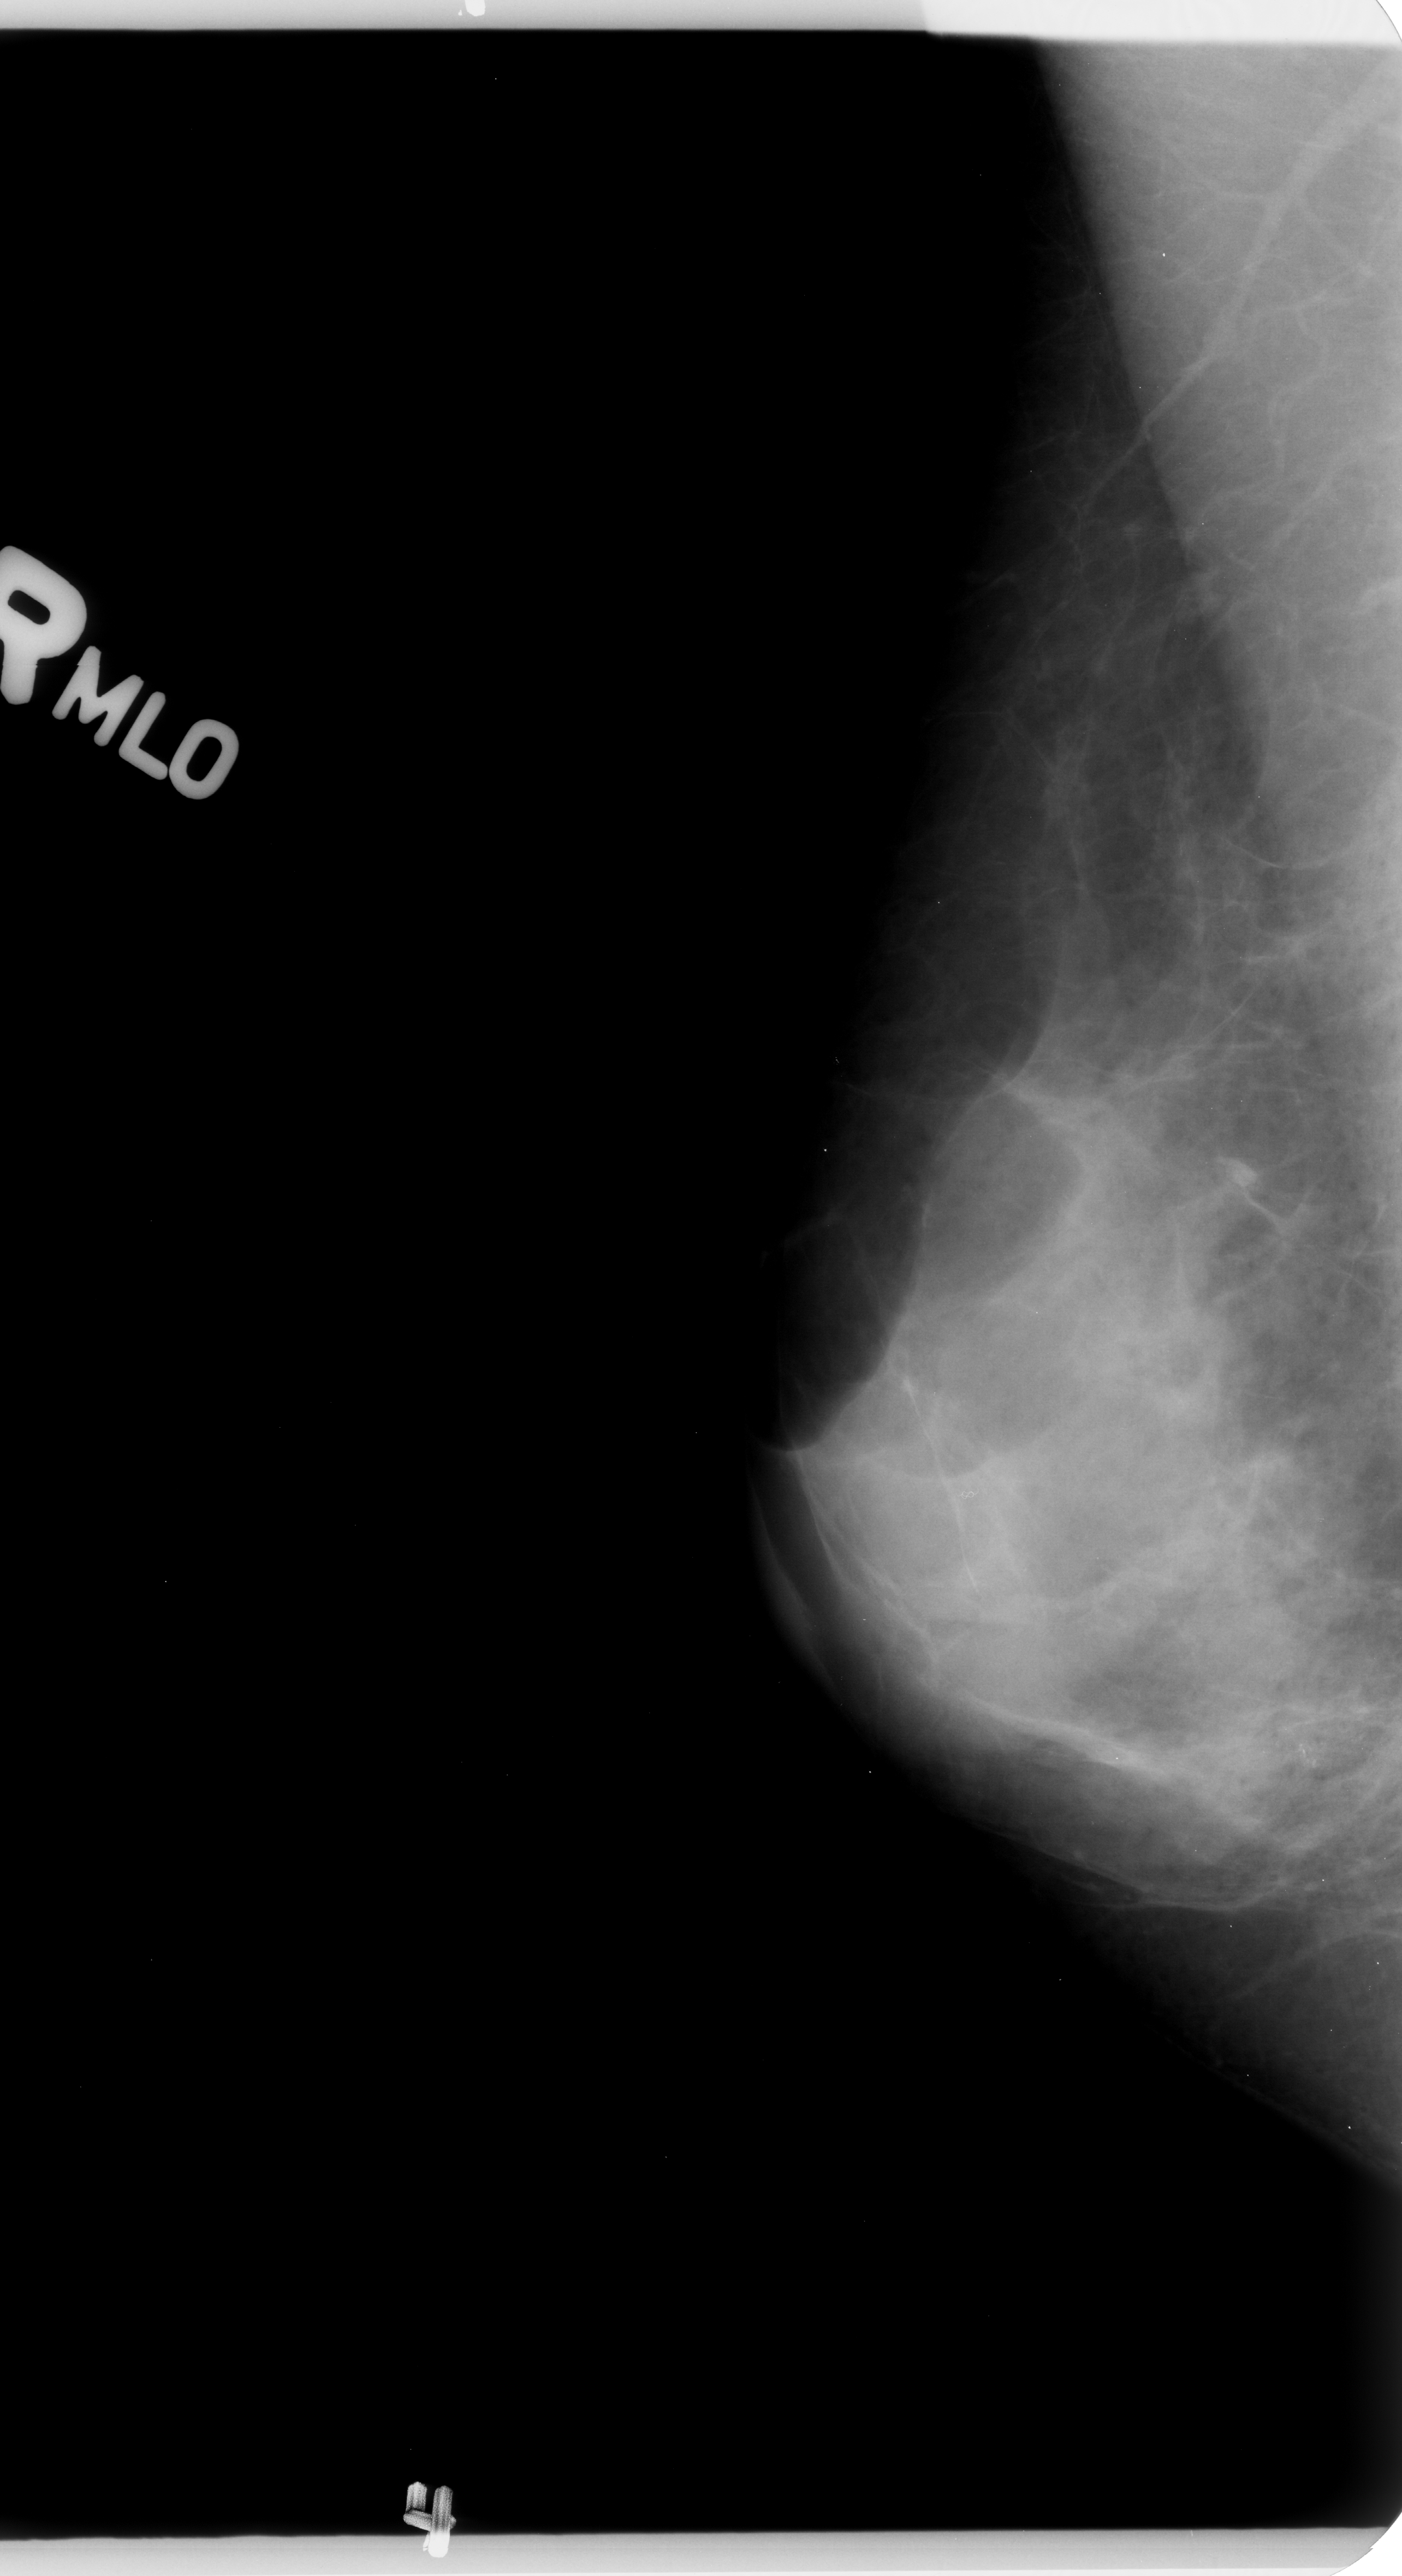
Mammogram (digitized film); right breast; mediolateral oblique (MLO) view; BI-RADS breast density category 4 (scale 1–4).
- Marked abnormality: calcifications, morphology pleomorphic, distribution clustered; BI-RADS assessment category 4; subtlety rating 3 on a 1 (subtle) to 5 (obvious) scale; pathology result (as recorded, not read from the image): benign.